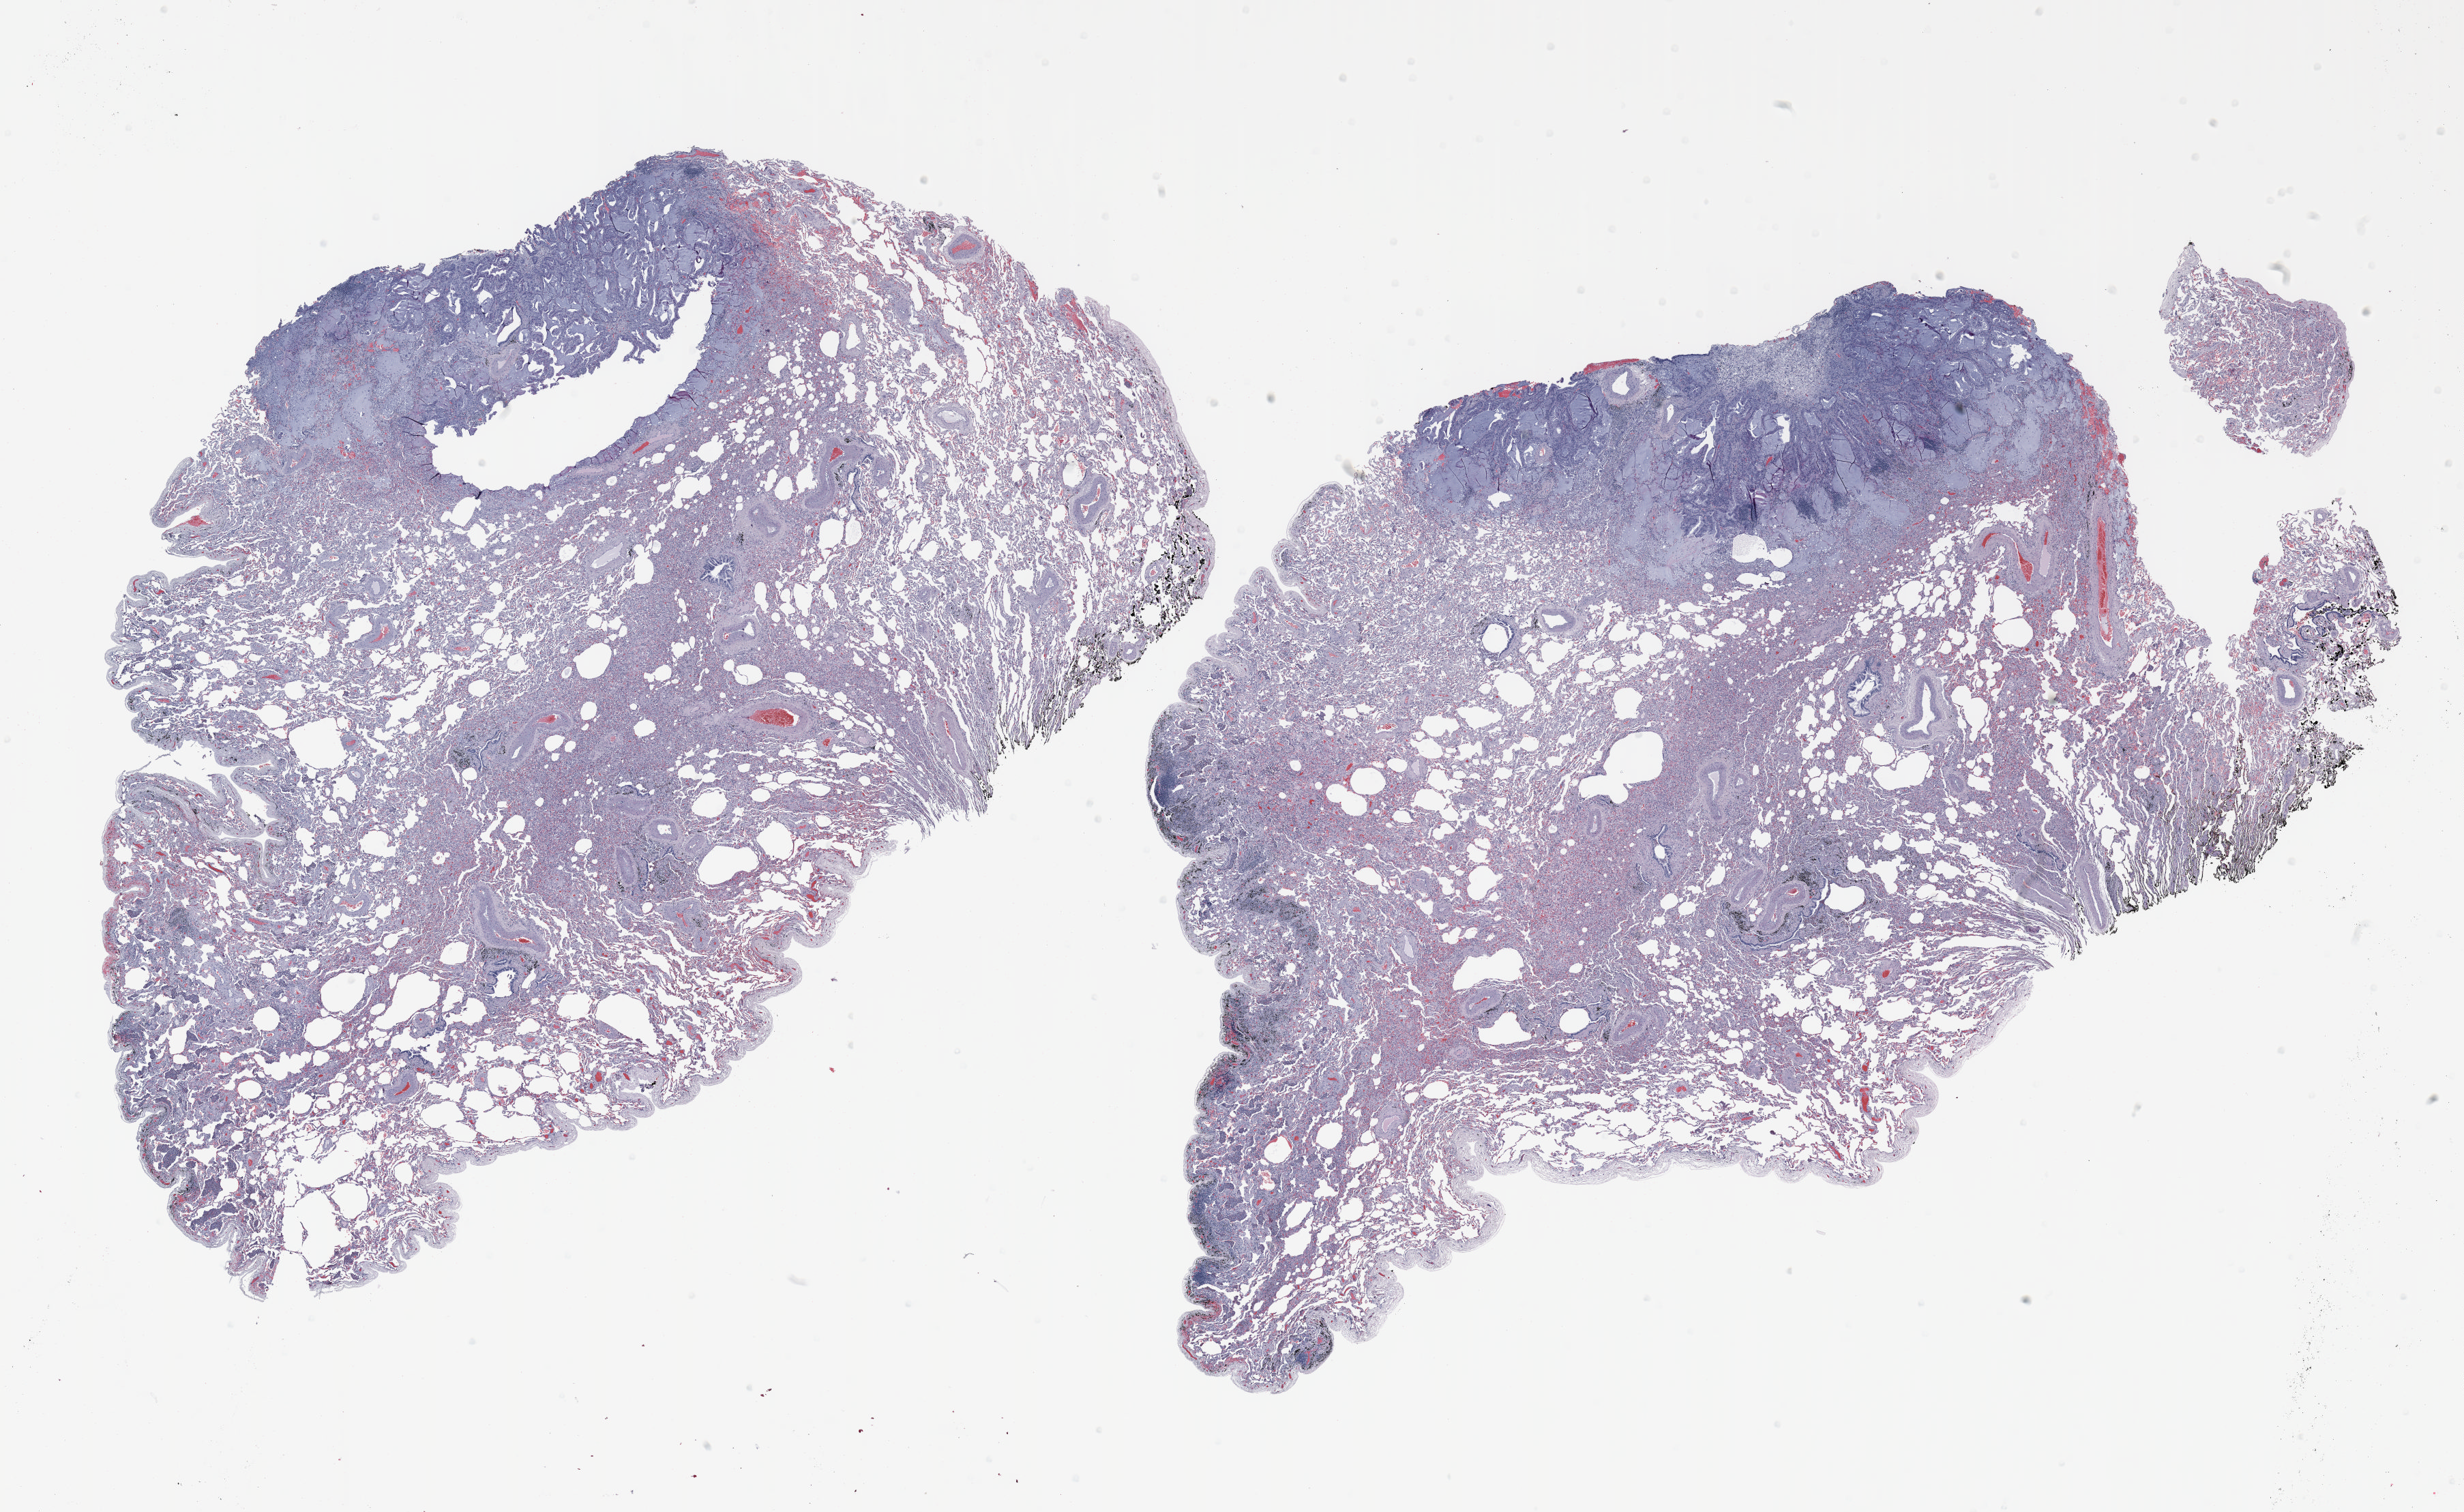
H&E whole-slide image, shown as a low-resolution overview of the whole scanned area (about 29.0 x 17.8 mm, slide scanned at 20x), FFPE section, lung. Male patient, aged 65 at enrolment. Former smoker at enrolment. Grade: well differentiated (G1).
- tumour size (pathology): 10 mm
- primary tumour location (clinical record): left lower lobe
- stage (AJCC 6th edition): IB
- ICD-O-3 topography: lower lobe of lung (C34.3)
- participant's lung-cancer diagnosis: Adenocarcinoma, NOS